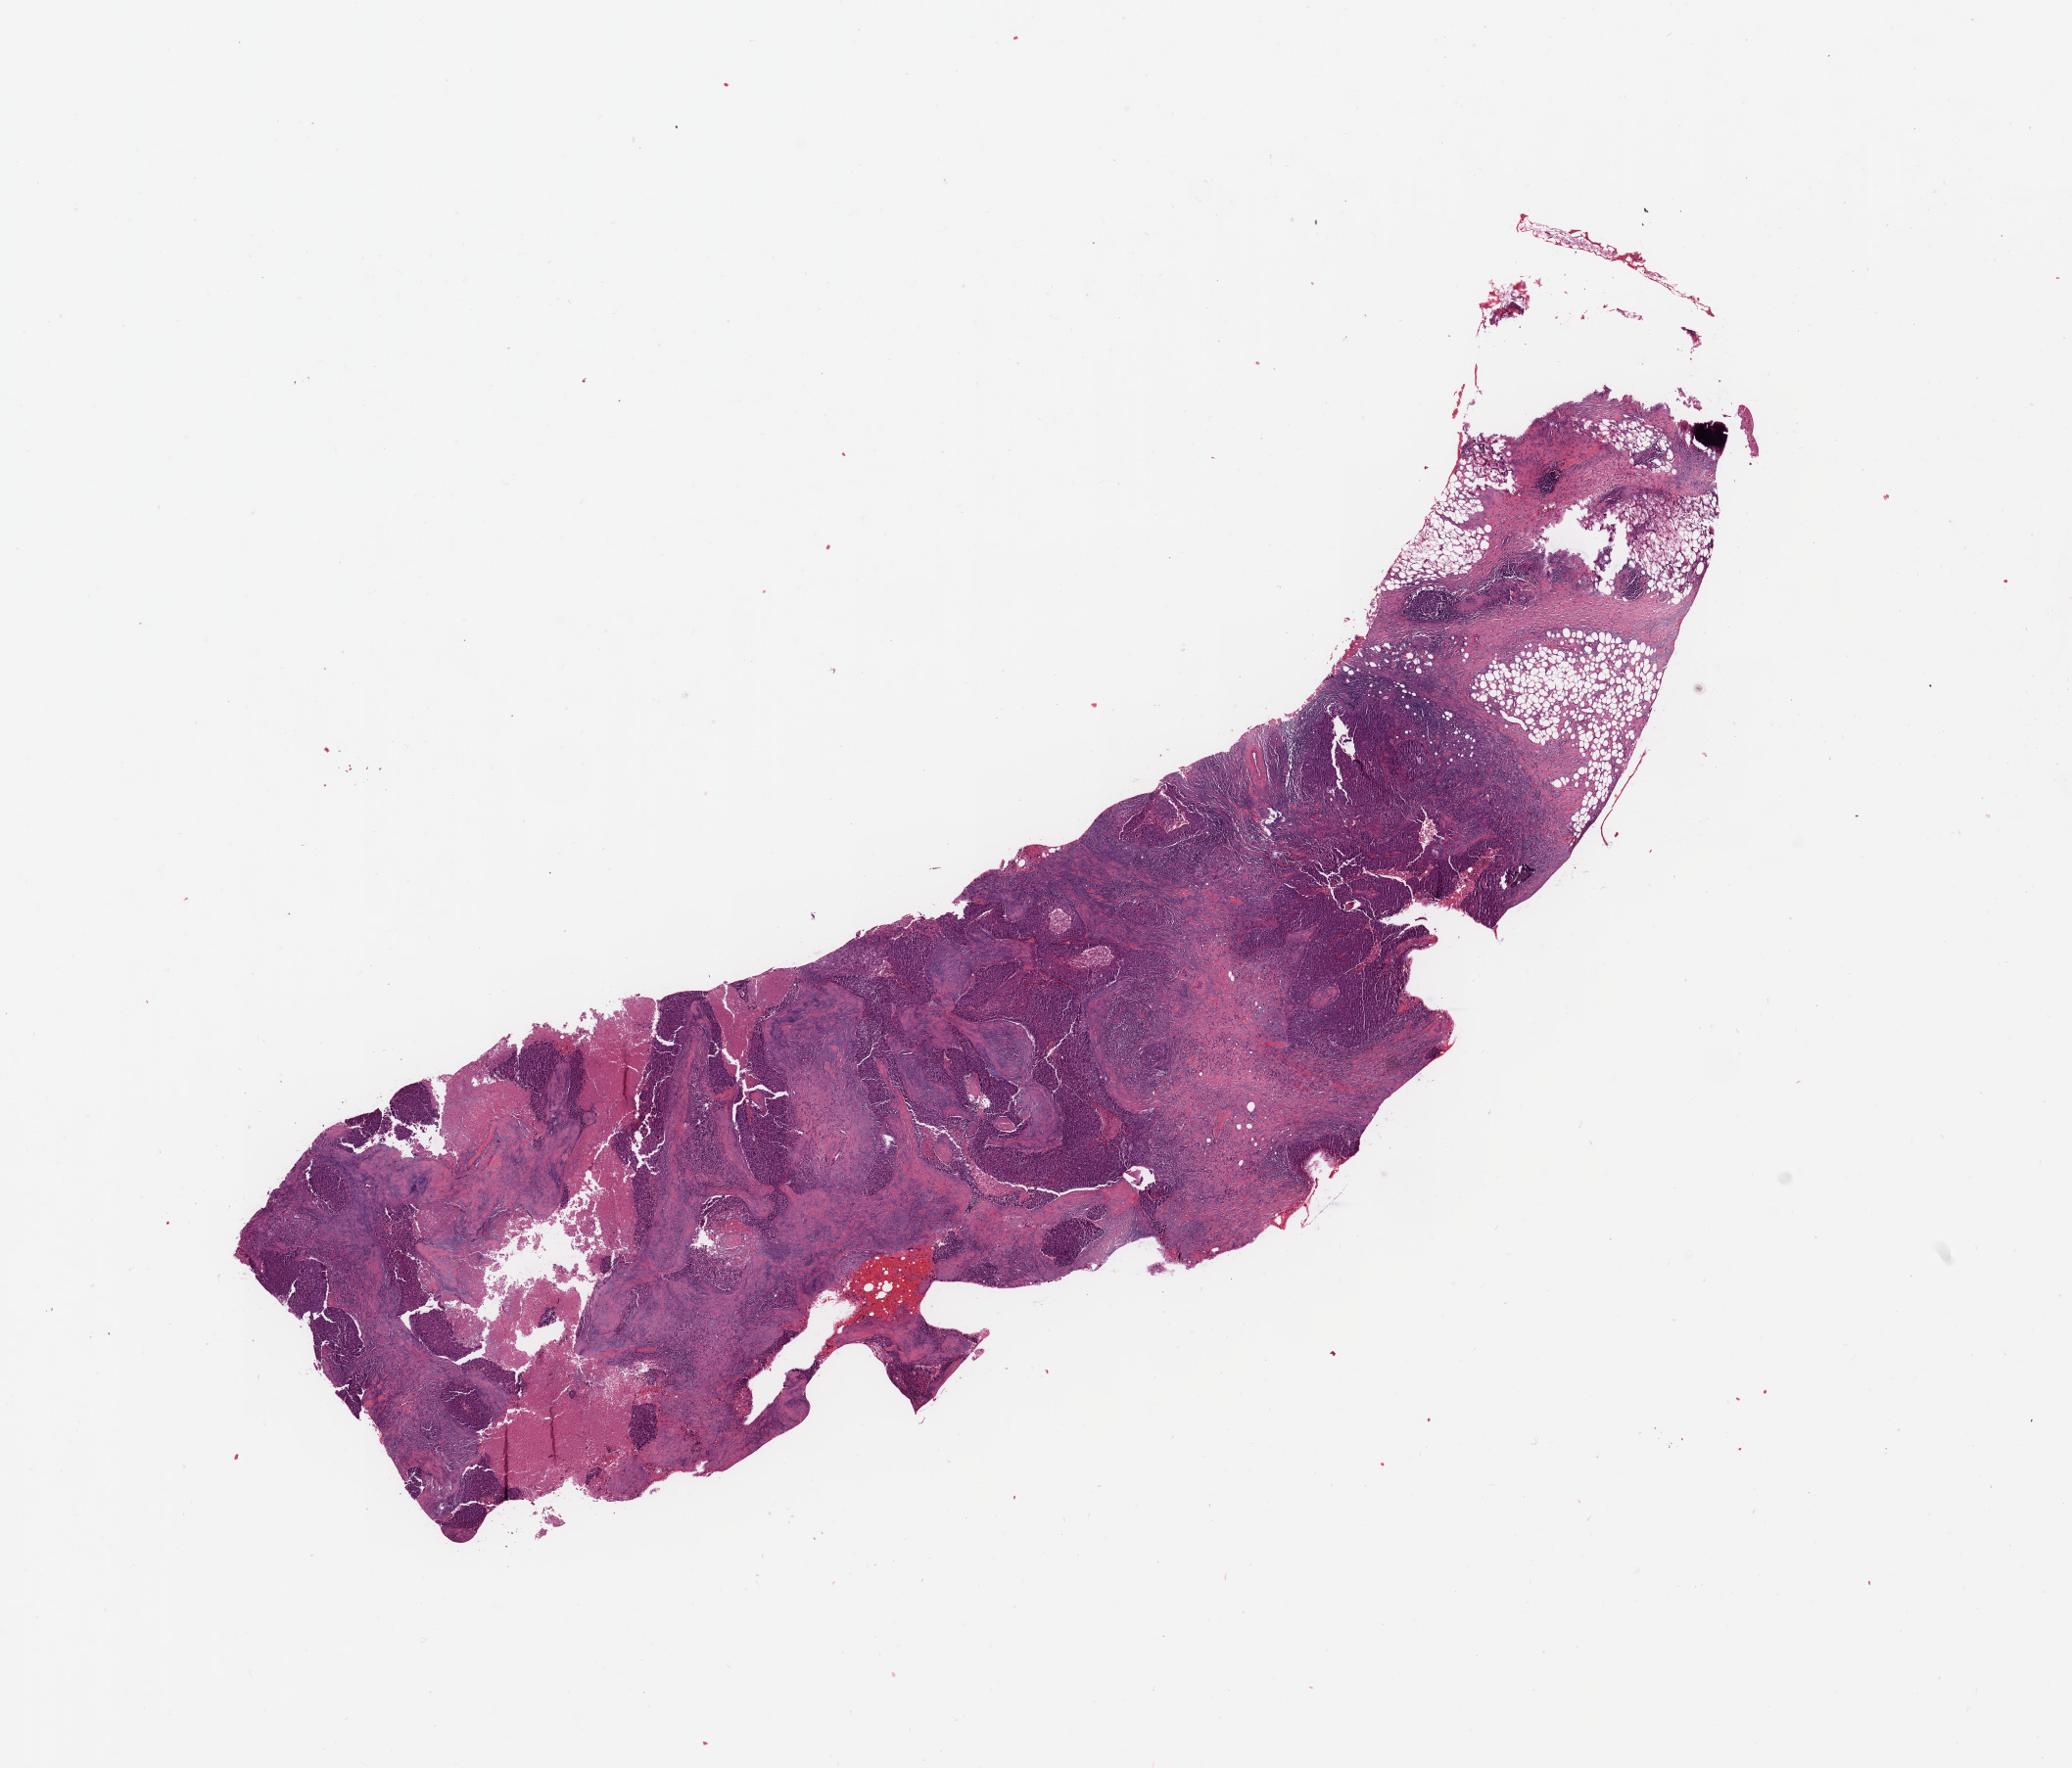
Whole-slide histology image, H&E-stained, low-resolution overview of the scanned area, about 16.7 x 14.3 mm (acquisition: 20x scan). Tumour tissue sample, lung. Patient: male, age 67 years.
Diagnosis: Squamous cell carcinoma, NOS.